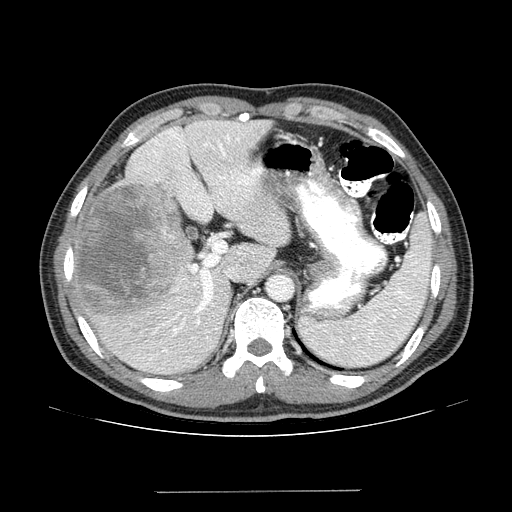
Contrast-enhanced abdominal CT (liver protocol), one axial slice; slice 96 of 131 in the series (ordered by position); reconstruction kernel STANDARD; 100 kVp; one of 2 acquisitions stored at this slice position; soft-tissue window (W 400 / L 40 HU); 512 × 512 image matrix, field of view 380 × 380 mm. Case-level facts recorded for this patient, not image findings: diagnosis: hepatocellular carcinoma (patient treated with transarterial chemoembolisation; whether this scan precedes or follows treatment is not stated here); TNM stage (as recorded): Stage-I; Child-Pugh class: A; tumour differentiation: poorly differentiated; tumour nodularity: uninodular.
Structures marked on this image (semi-automatic segmentation, software-assisted and operator-edited):
- liver parenchyma outside the tumour (the mass and vessels are separate outlines, so this box may not span the whole liver): bounding box (x1, y1, x2, y2) in pixels: (70, 120, 290, 374)
- mass: (75, 184, 191, 320)
- liver vessels: (70, 129, 263, 370)